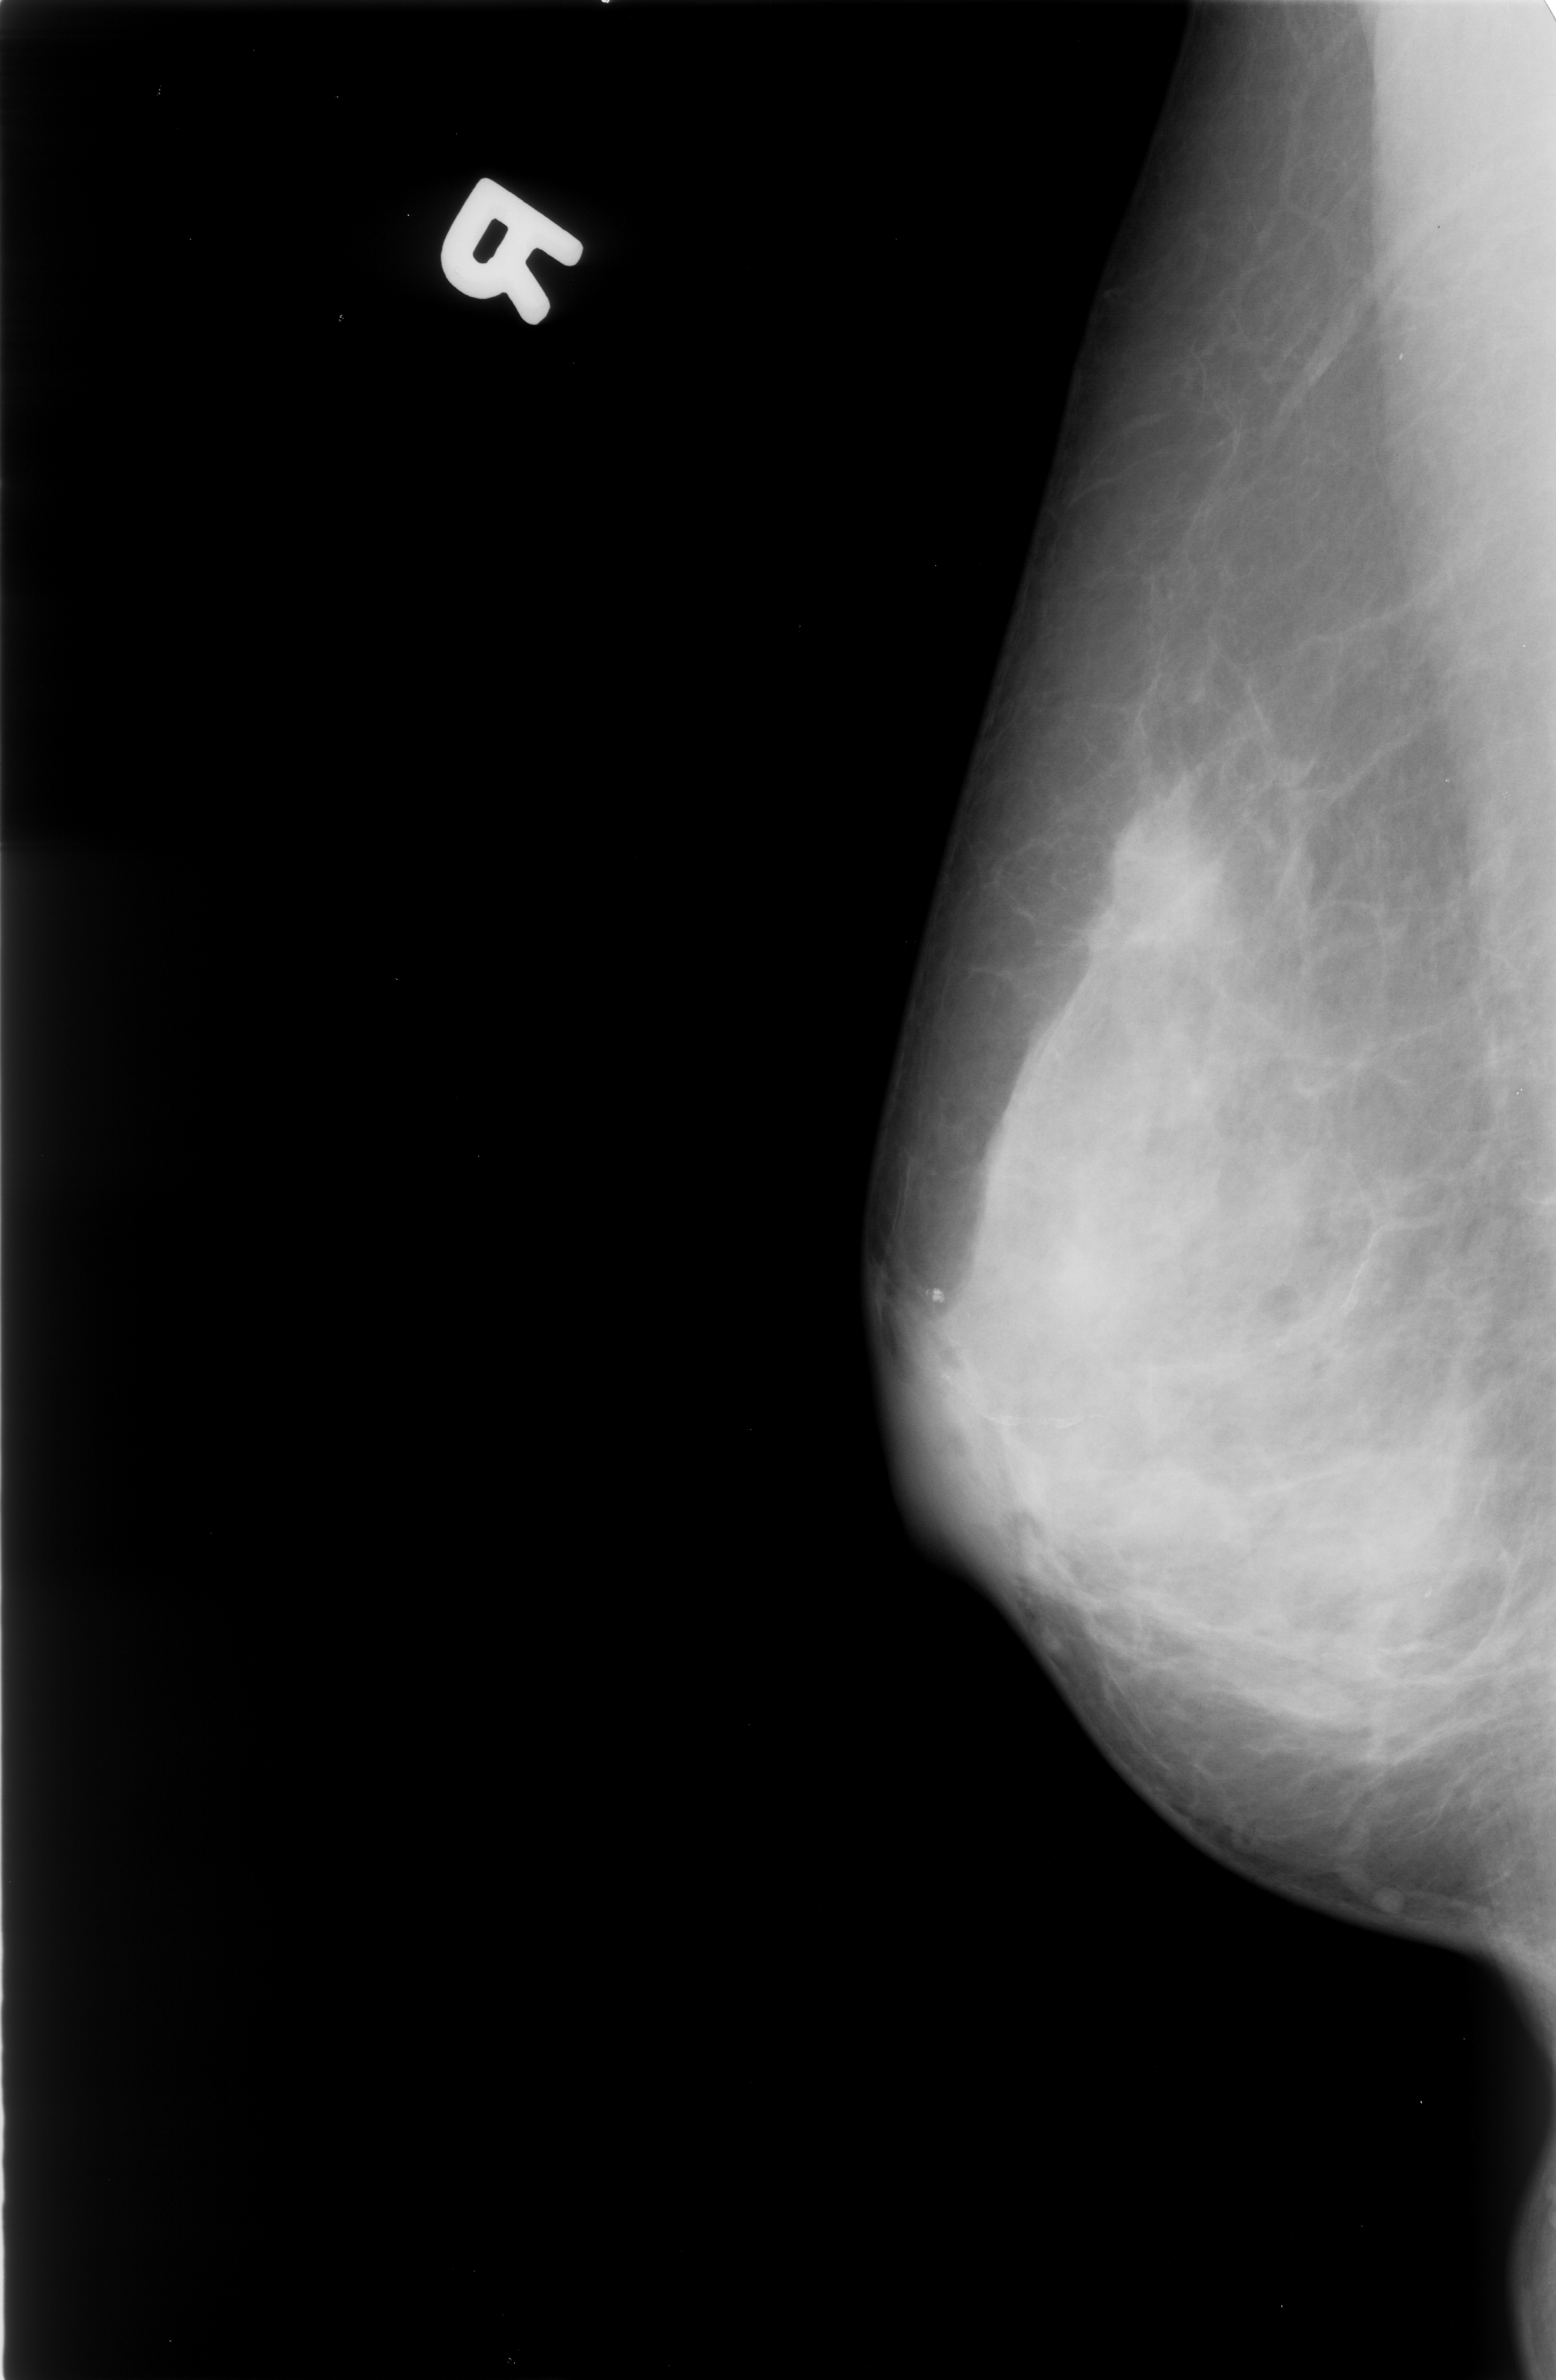
Digitized screen-film mammogram, right breast, MLO view, BI-RADS breast density category 4 (scale 1–4).
Marked abnormality: mass, shape irregular / architectural distortion, margins obscured / ill defined; BI-RADS assessment category 4; pathology result (as recorded, not read from the image): malignant.